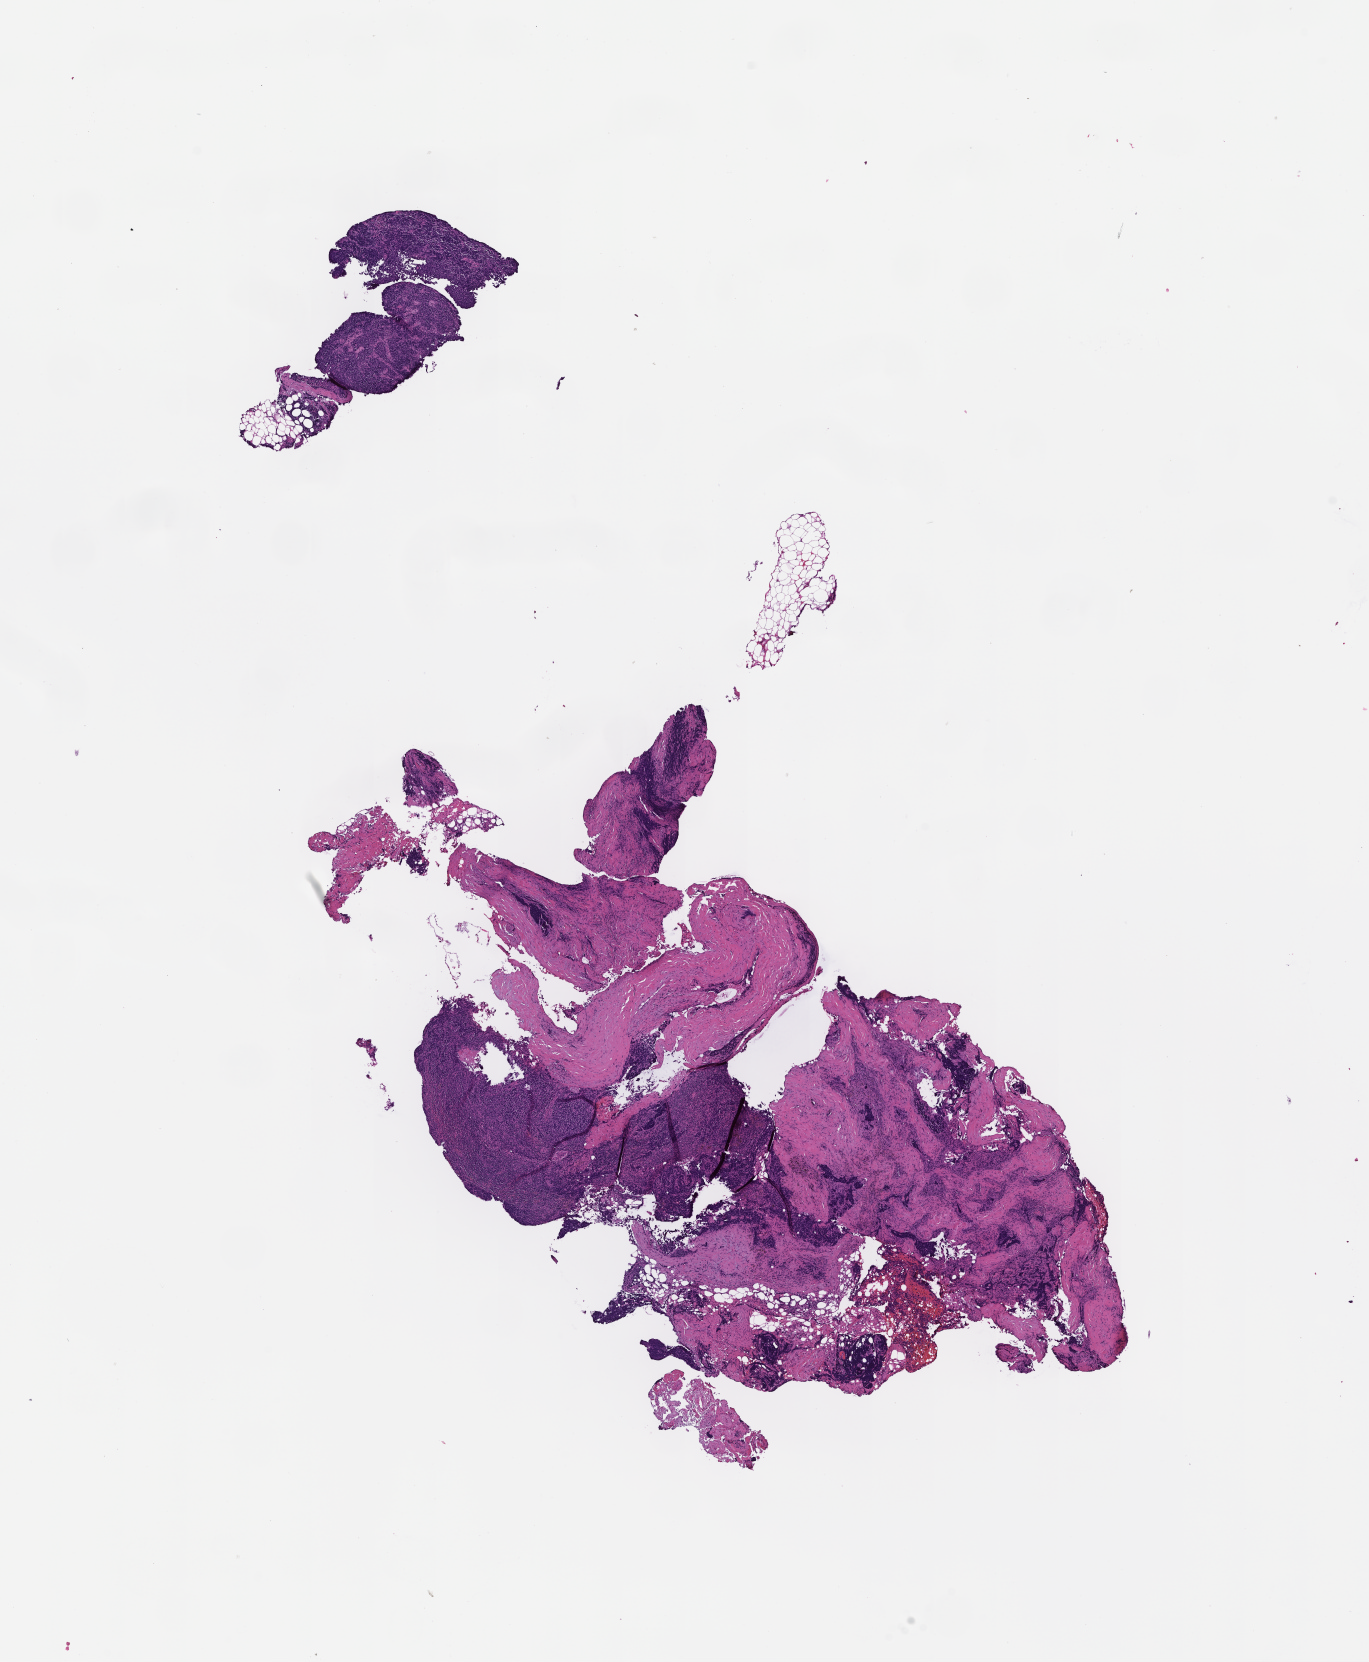
Digitized hematoxylin and eosin (H&E)-stained section, low-resolution overview of the scanned area, about 11.1 x 13.4 mm, FFPE section, specimen time point: archival tissue. Patient: male.
This section: metastatic tumor tissue. Patient diagnosis (primary): Small Cell Lung Carcinoma.